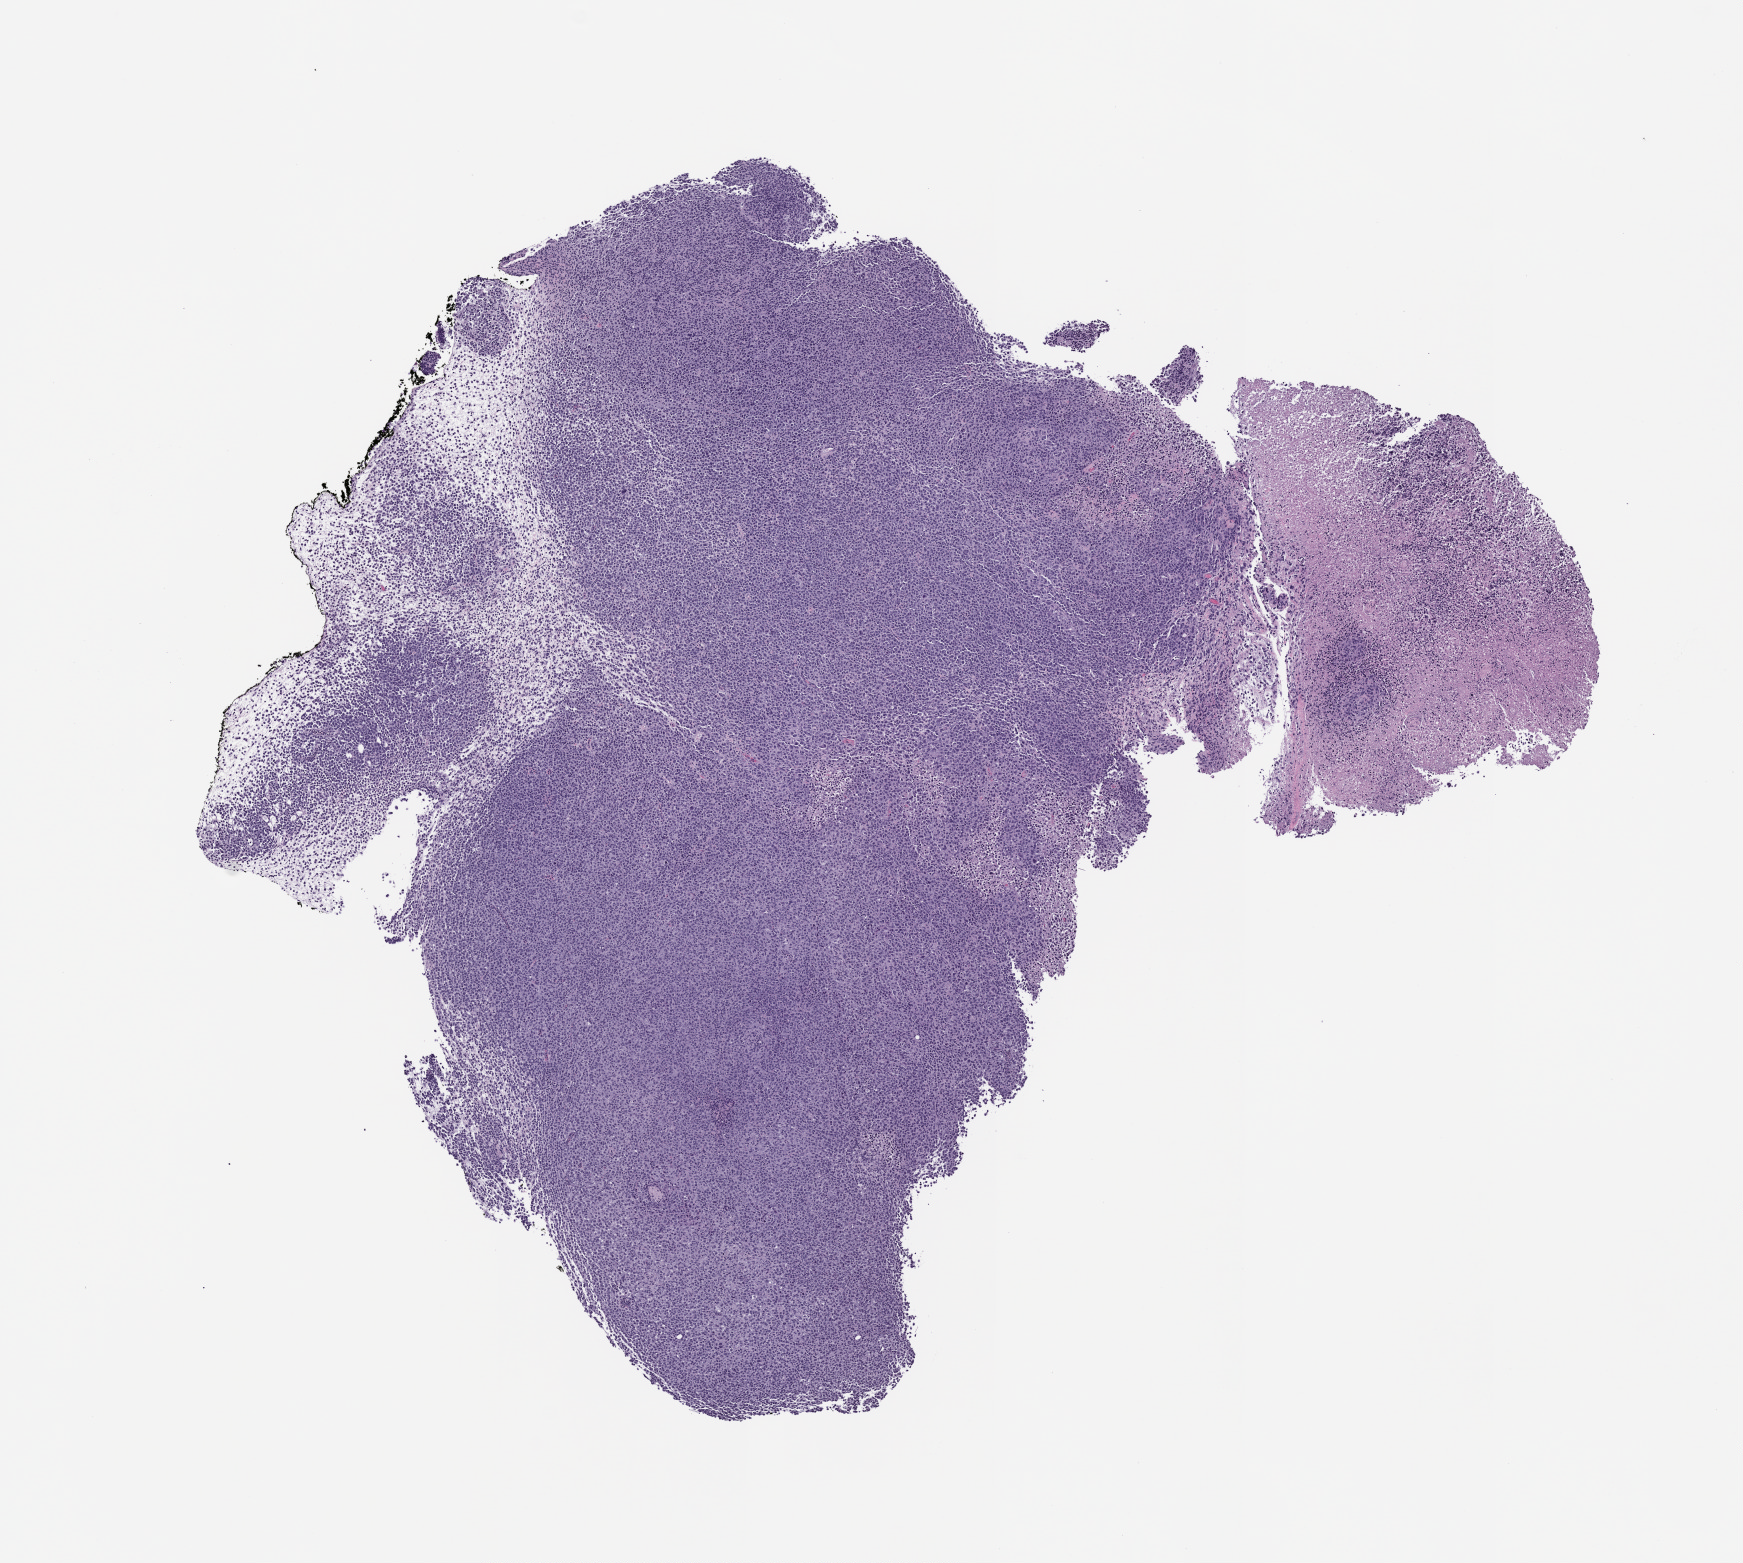
Hematoxylin and eosin (H&E) whole-slide image of a patient-derived xenograft (PDX) tumor grown in a mouse, a low-resolution overview of the entire scanned area, about 7.0 x 6.3 mm.
Specimen: FFPE section.